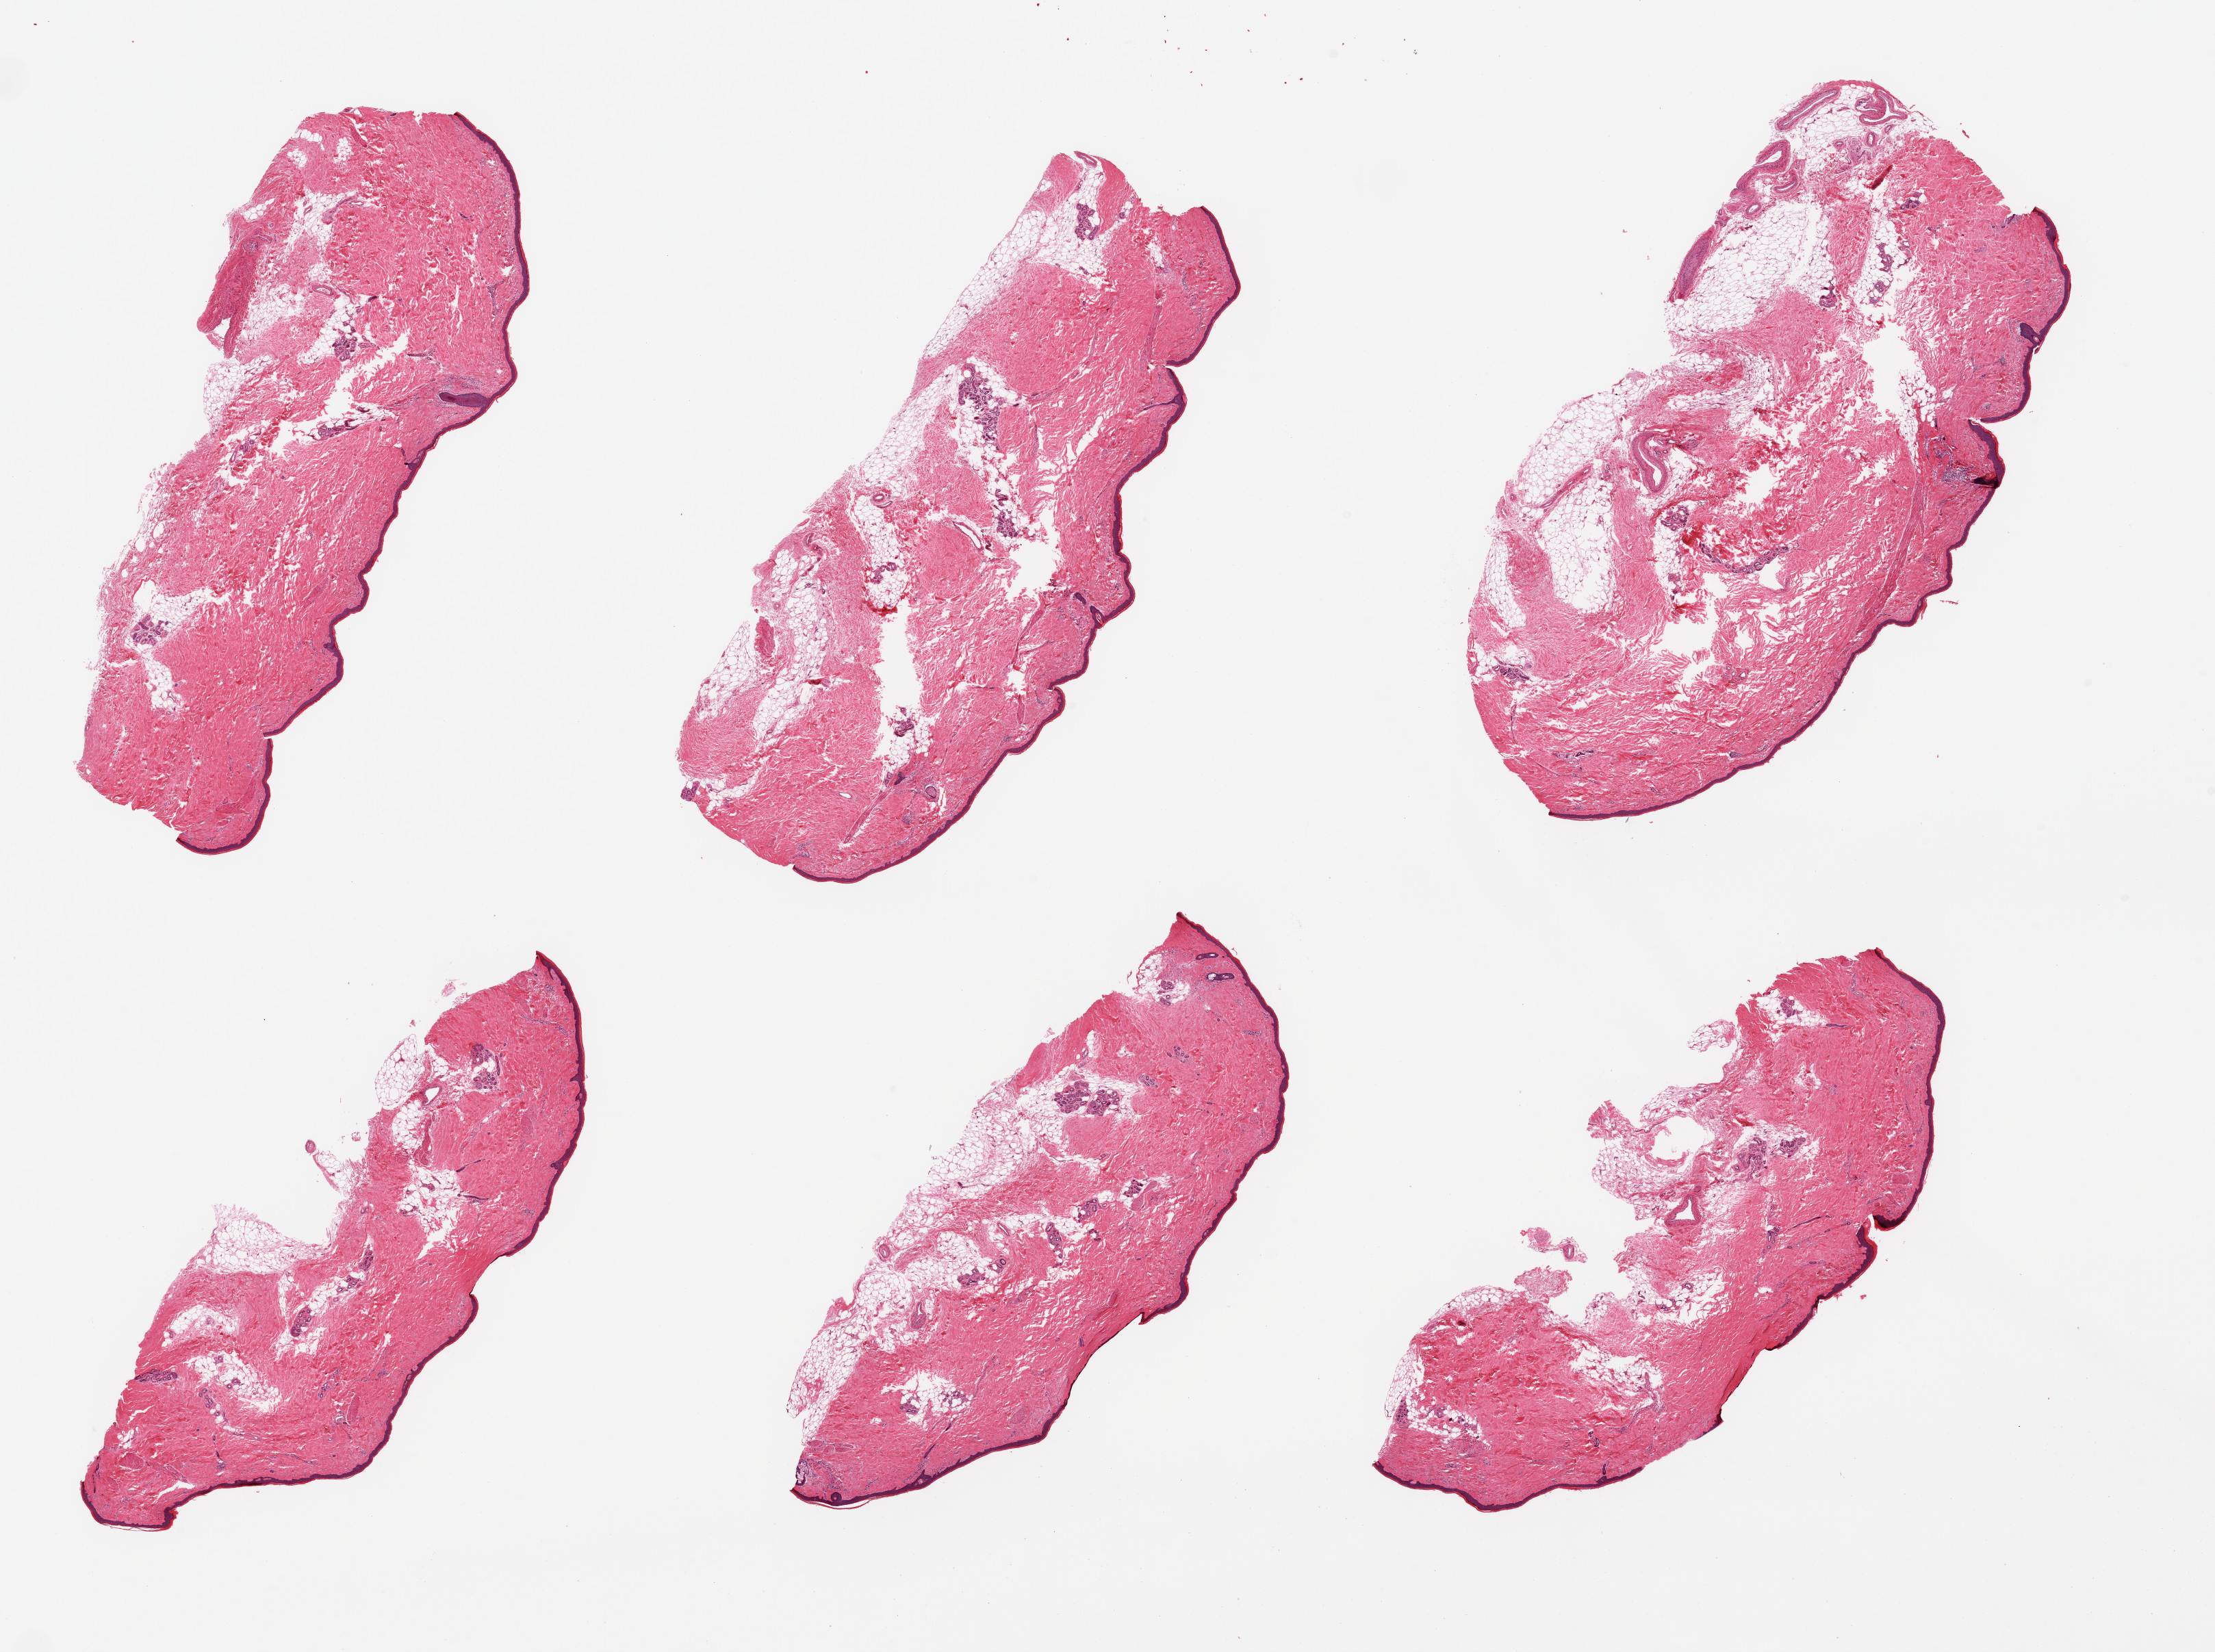
Whole-slide image, haematoxylin and eosin stain, brightfield — a low-resolution overview of the entire scanned area, about 25.6 x 19.1 mm, PAXgene-fixed paraffin-embedded (PFPE) section, section of skin of lower leg (target tissue), donor tissue sample. Donor: male.
Reviewer comment on this tissue sample: 6 pieces, adherent dermal fat up to ~0.7mm; squamous epithelium is ~50-60 microns.